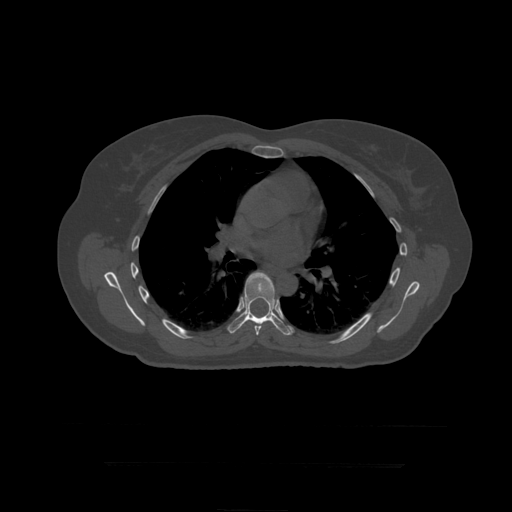
CT including the spine, one axial slice. Slice 289 of 399 in the series (ordered by position). 120 kVp. Bone window (W 1800 / L 400 HU). 512 × 512 image matrix, field of view 450 × 450 mm. Patient age 41 years. From the clinical record (not read from this slice): primary cancer: breast.
Annotated regions visible in this slice (semi-automatic segmentation, software-assisted and operator-edited):
- T7 vertebra: bounding box <254,273,271,336> (left, top, right, bottom; pixels)
- T8 vertebra: <227,272,291,336>